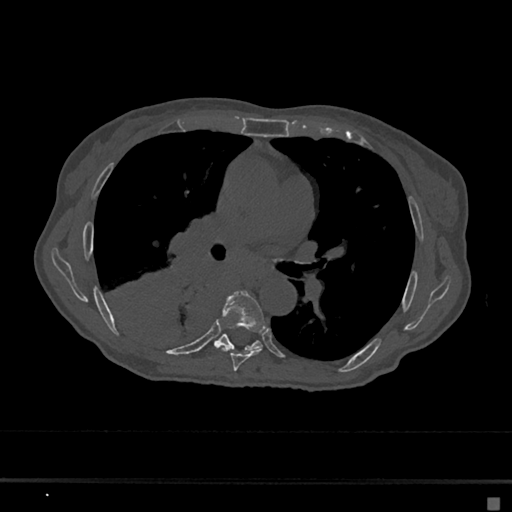
CT including the spine, one axial slice. Slice 399 of 797 in the series (ordered by position). Reconstruction kernel Br40s/3. 120 kVp. Bone window (W 1800 / L 400 HU). 0.5 mm slice thickness. 512 × 512 image matrix, field of view 360 × 360 mm. Patient: female, 68 years. Case-level facts recorded for this patient, not image findings: primary cancer: renal.
Outlined on this slice (semi-automatically segmented with operator editing):
- T6 vertebra: bounding box [x1, y1, x2, y2] px = [222, 290, 267, 371]
- T7 vertebra: [213, 334, 263, 351]